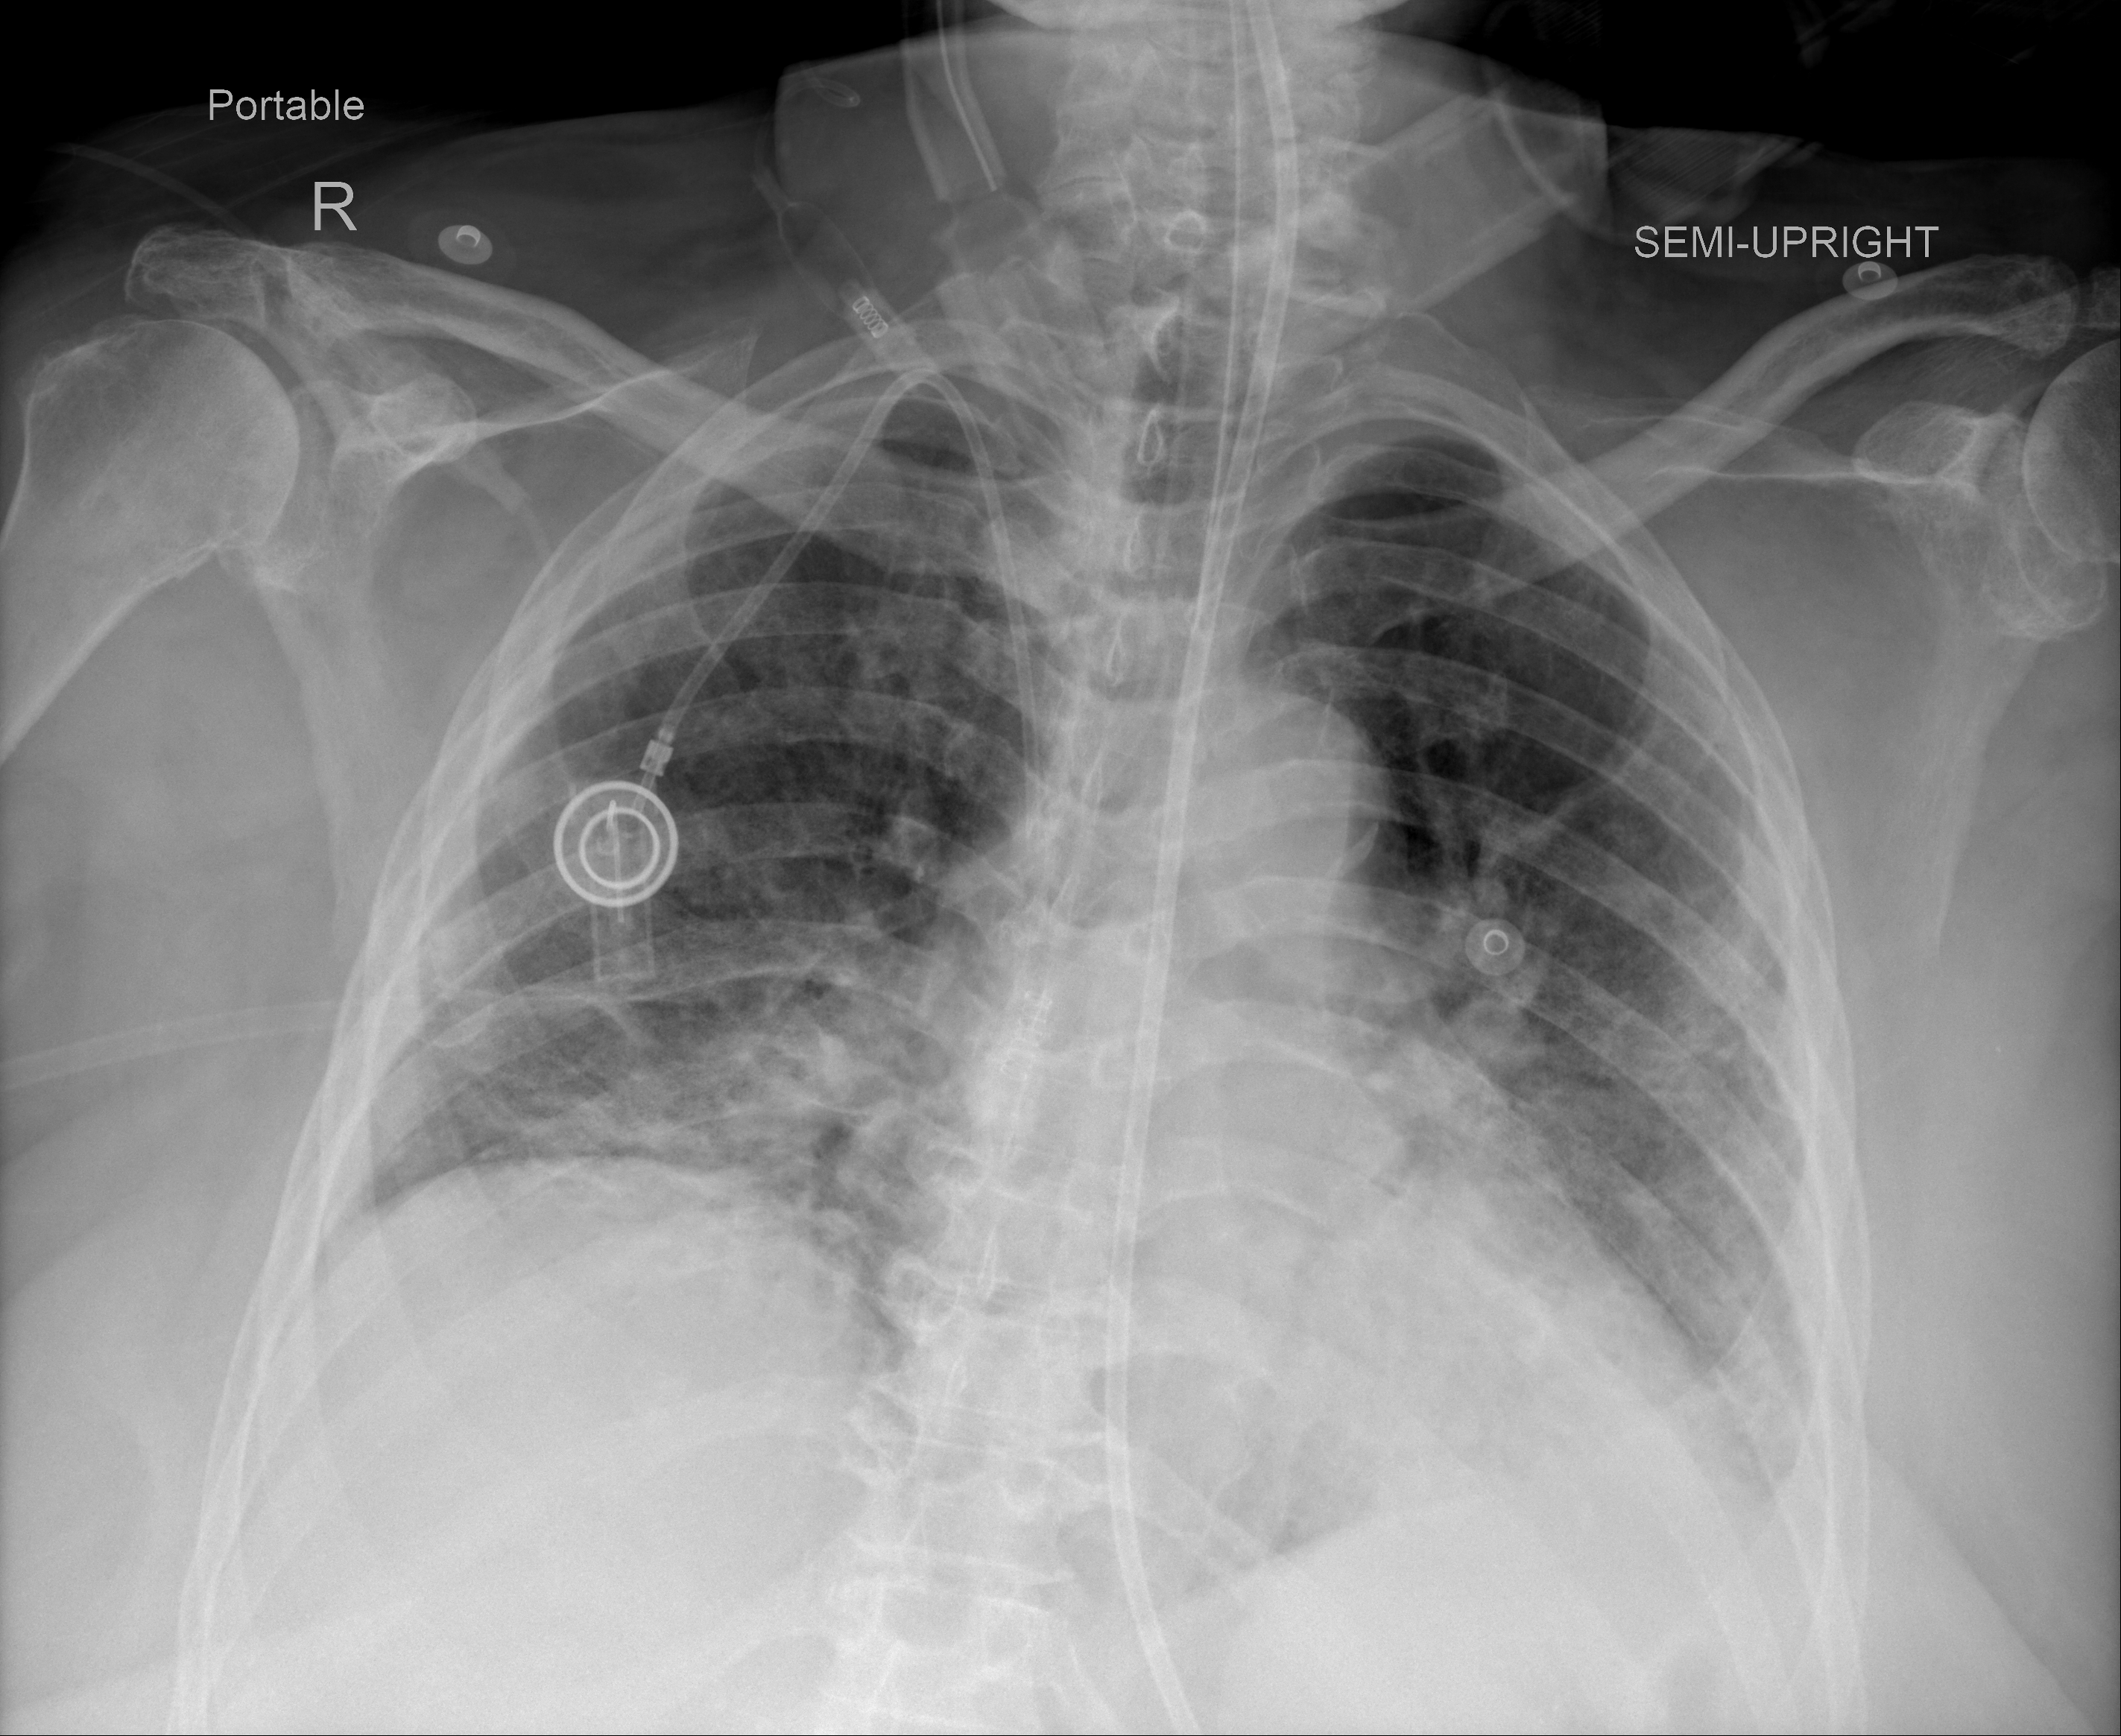
Chest X-ray (portable), AP projection. Female patient, age 76 years; imaged 6 days after the COVID-19 diagnosis.
Key findings recorded by the radiologist: Persistent bilateral airspace disease but perhaps slight improvement.